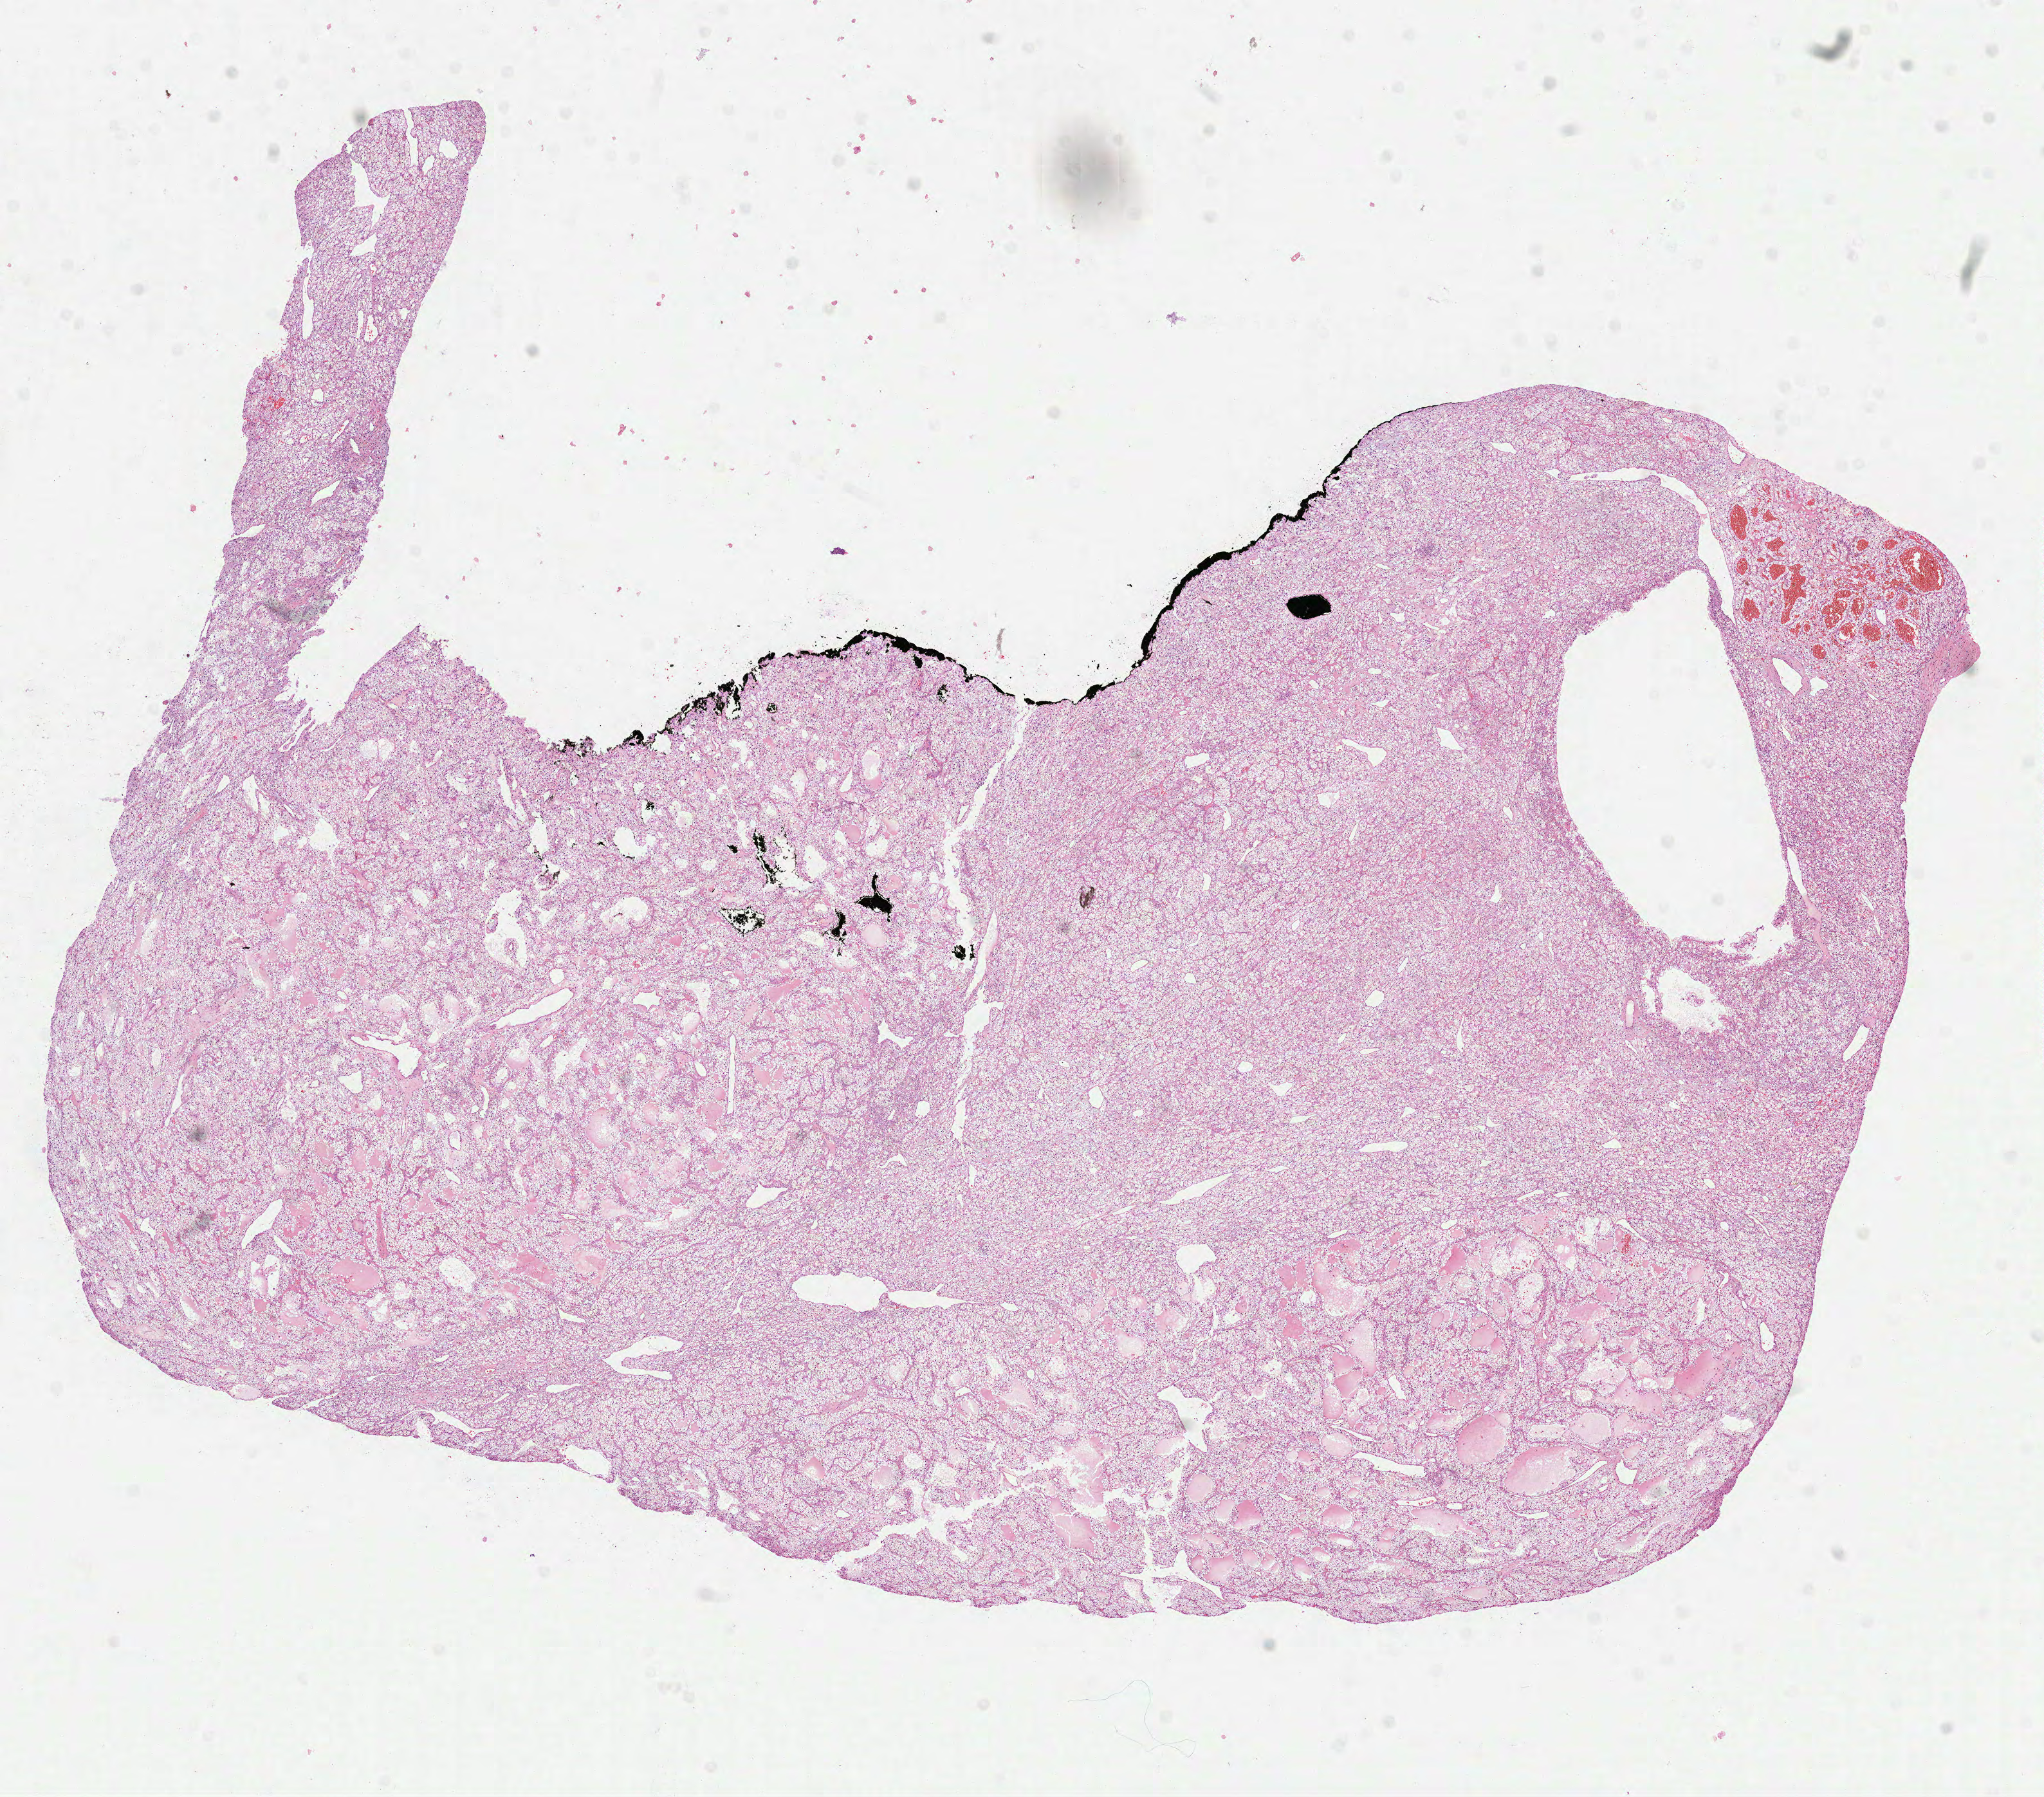
Hematoxylin and eosin (H&E) stained whole-slide image, low-resolution overview of the scanned area, about 12.8 x 11.3 mm (from a 40x scan). Formalin-fixed paraffin-embedded (FFPE) diagnostic section. Primary tumour sample from the kidney. Male patient; age at initial diagnosis 57 years. Histologic grade: G2 (moderately differentiated).
AJCC pathologic stage: I. Histologic diagnosis: Clear cell adenocarcinoma, NOS. Laterality: right.